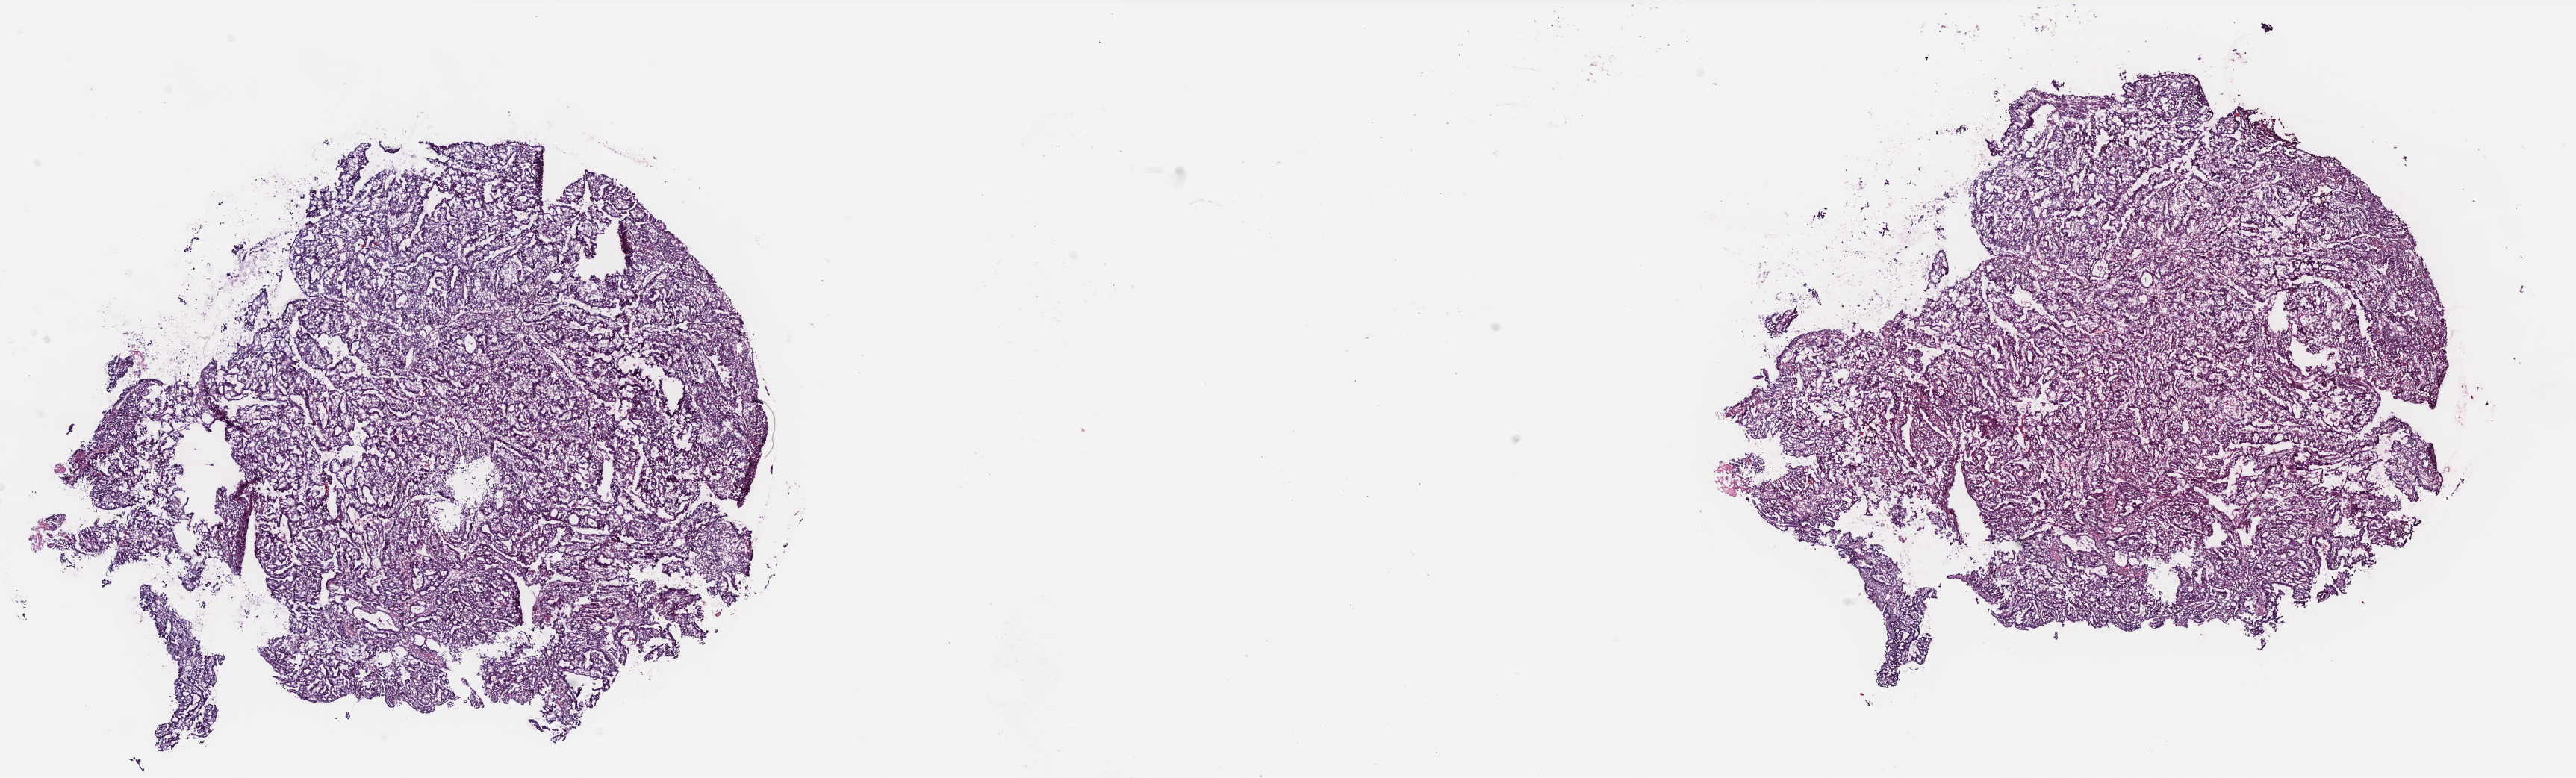
Whole-slide histology image, H&E-stained, shown as a low-resolution overview of the whole scanned area (about 27.7 x 8.4 mm, slide scanned at 40x), frozen section from the bottom of the tissue portion, primary tumour sample from the rectum. Male, age 35 years at initial diagnosis. Slide review estimates, as recorded: tumour cells 99%, tumour nuclei 80%, normal cells 0%, stromal cells 0%, necrosis 1%. Inflammatory infiltration, as recorded: lymphocyte infiltration 1%, monocyte infiltration 2%, neutrophil infiltration 5%.
AJCC pathologic stage: I (6th edition). Diagnosis: Adenocarcinoma, NOS. Lymph nodes positive (case pathology): 0 of 34 examined. TNM: T2 N0 M0.